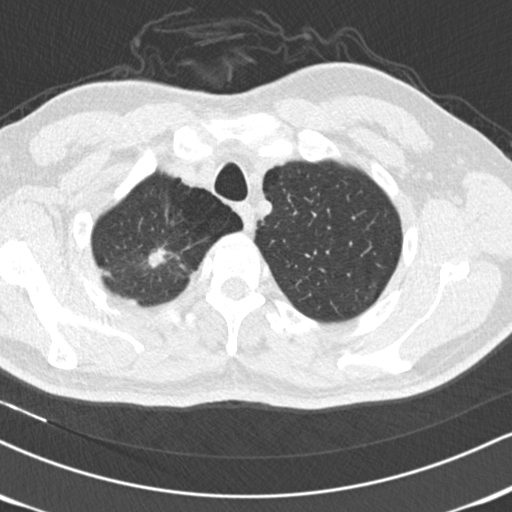
Axial slice from a low-dose chest CT screening exam; second annual screen; lung window (W 1500 / L -600 HU); slice 29 of 179 in the series; 512 × 512 image matrix. Male, age 56 years at enrolment. Former smoker at enrolment.
Lesion marked by an expert reader, bounding box (x1, y1, x2, y2) in pixels: (126, 236, 186, 282). The exam's reader record, not a measurement of the box and not confirmed to be the same lesion: non-calcified nodule or mass ≥4 mm, right upper lobe, 13 × 10 mm, spiculated (stellate) margins, soft tissue attenuation. Official screen result: positive, other.